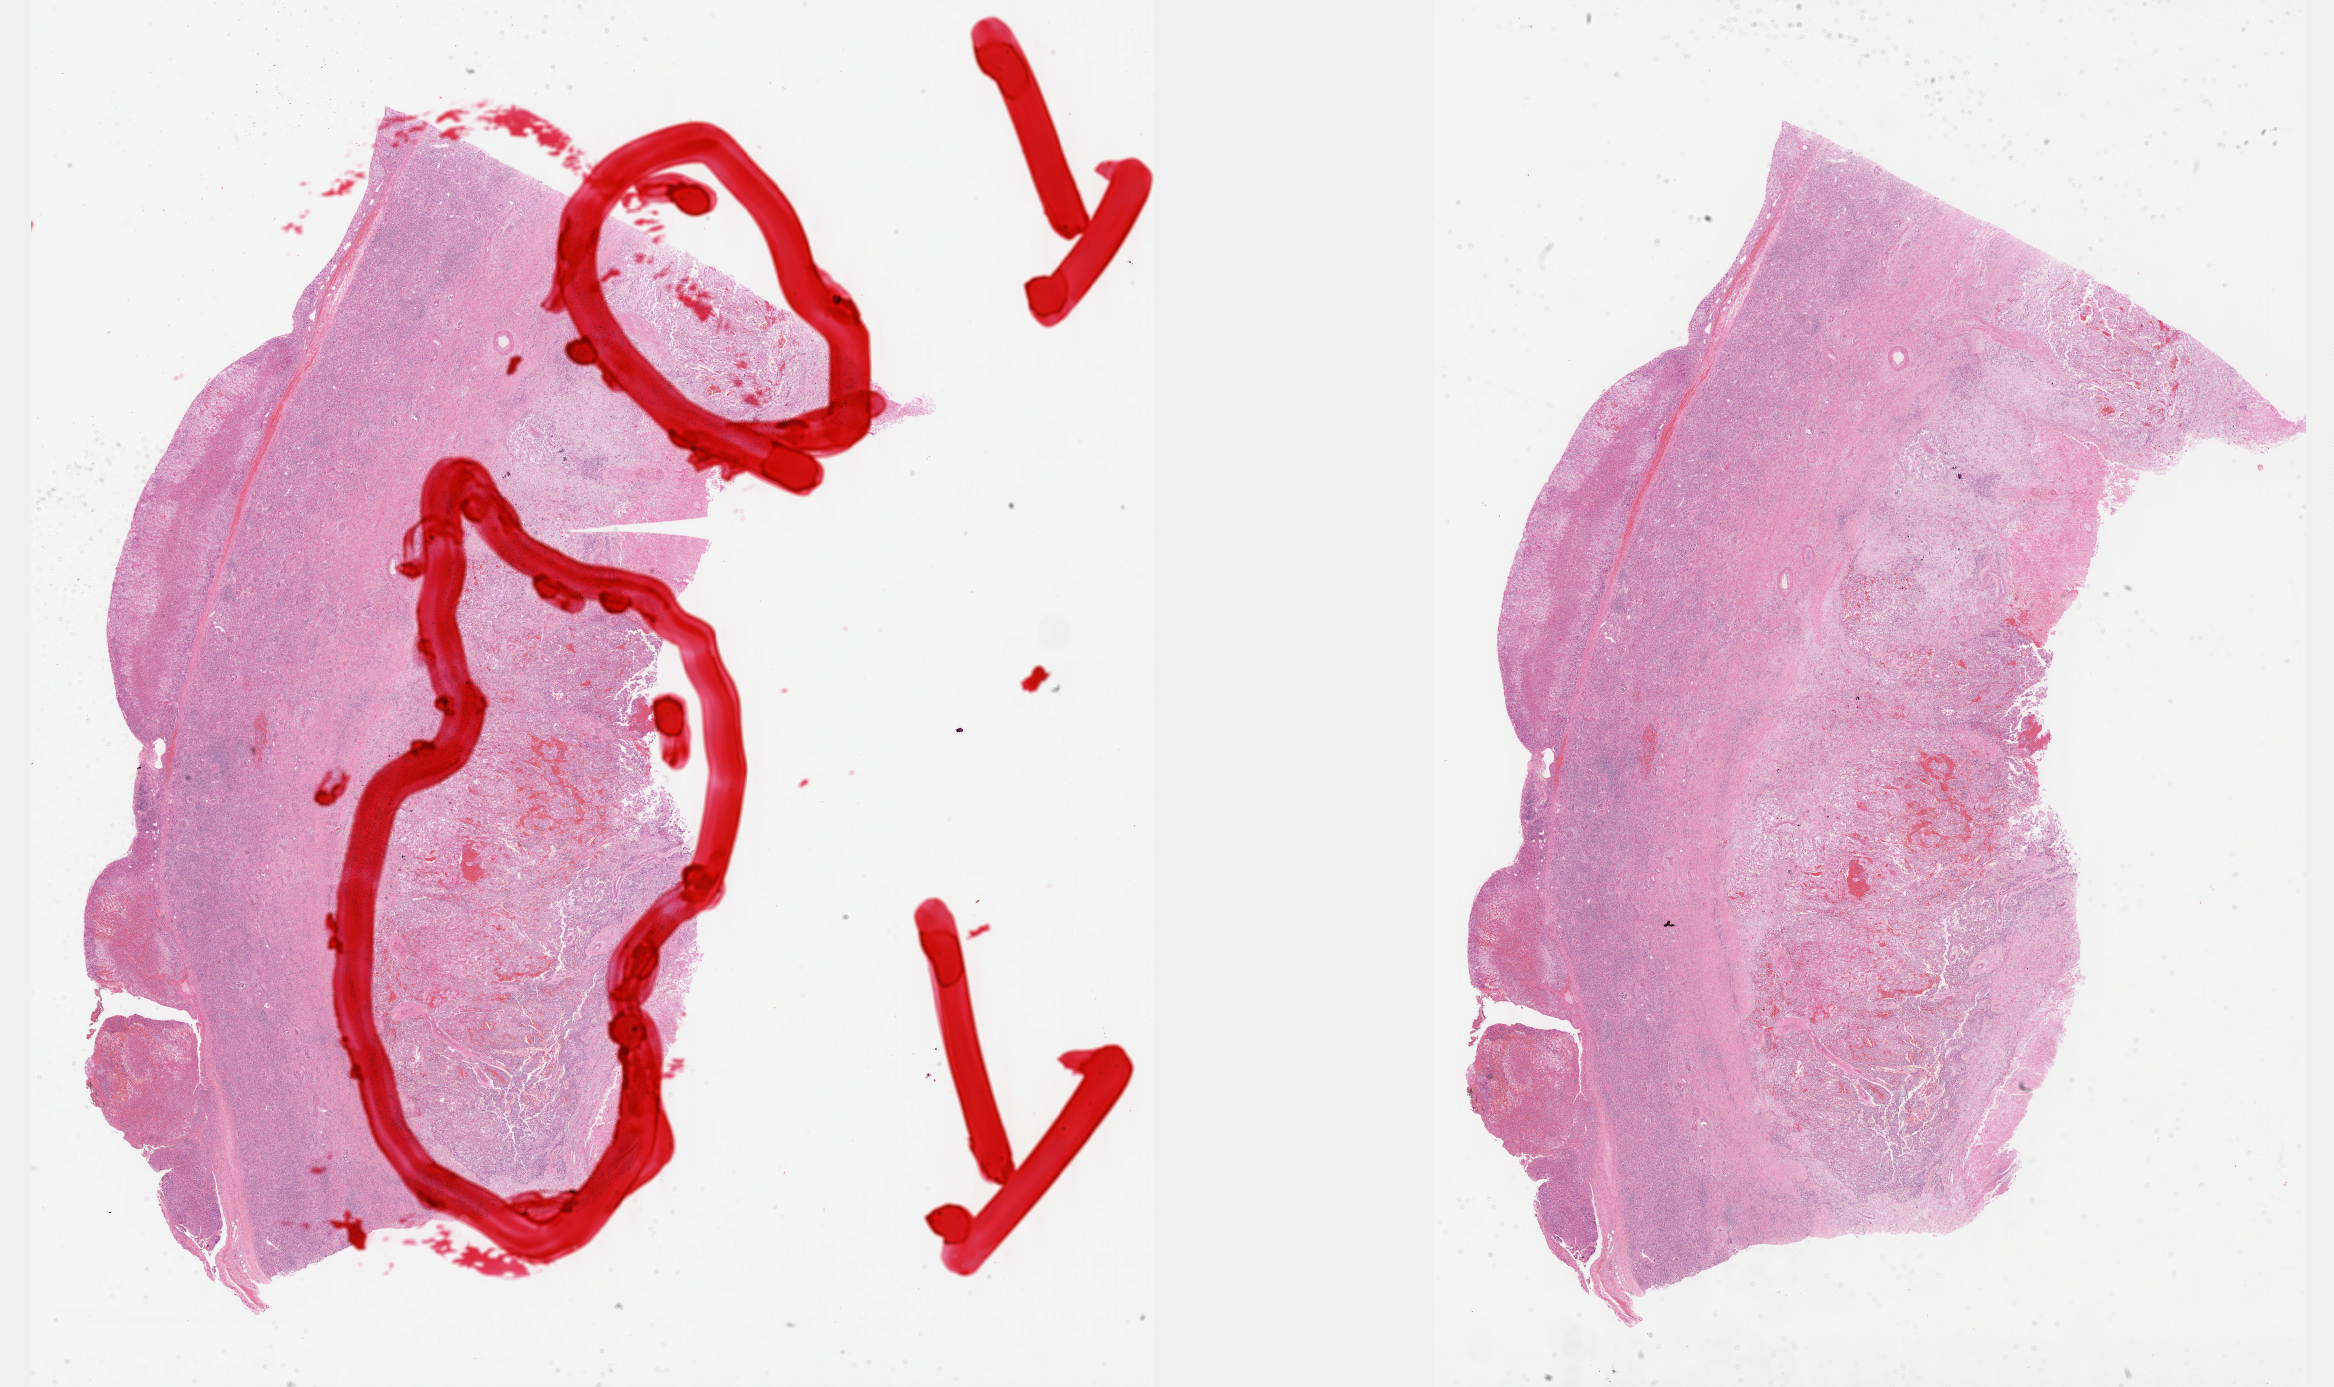
Digitized Hematoxylin and eosin (H&E) stained tissue section (whole slide), whole scanned area (about 37.7 x 22.4 mm) shown as a low-resolution overview; formalin-fixed paraffin-embedded (FFPE) diagnostic section; primary tumour sample from the kidney. Female, age 33 years at initial diagnosis. Composition of this section per pathologist review: tumour cells 75%, tumour nuclei 87%, normal cells 0%, stromal cells 25%, necrosis 0%. Inflammatory infiltration, as recorded: lymphocyte infiltration 8%, monocyte infiltration 4%, neutrophil infiltration 0%.
TNM: T1a N0. Histologic diagnosis: Renal cell carcinoma, chromophobe type. AJCC pathologic stage: I (6th edition). Lymph nodes positive (case pathology): 0 of 1 examined.